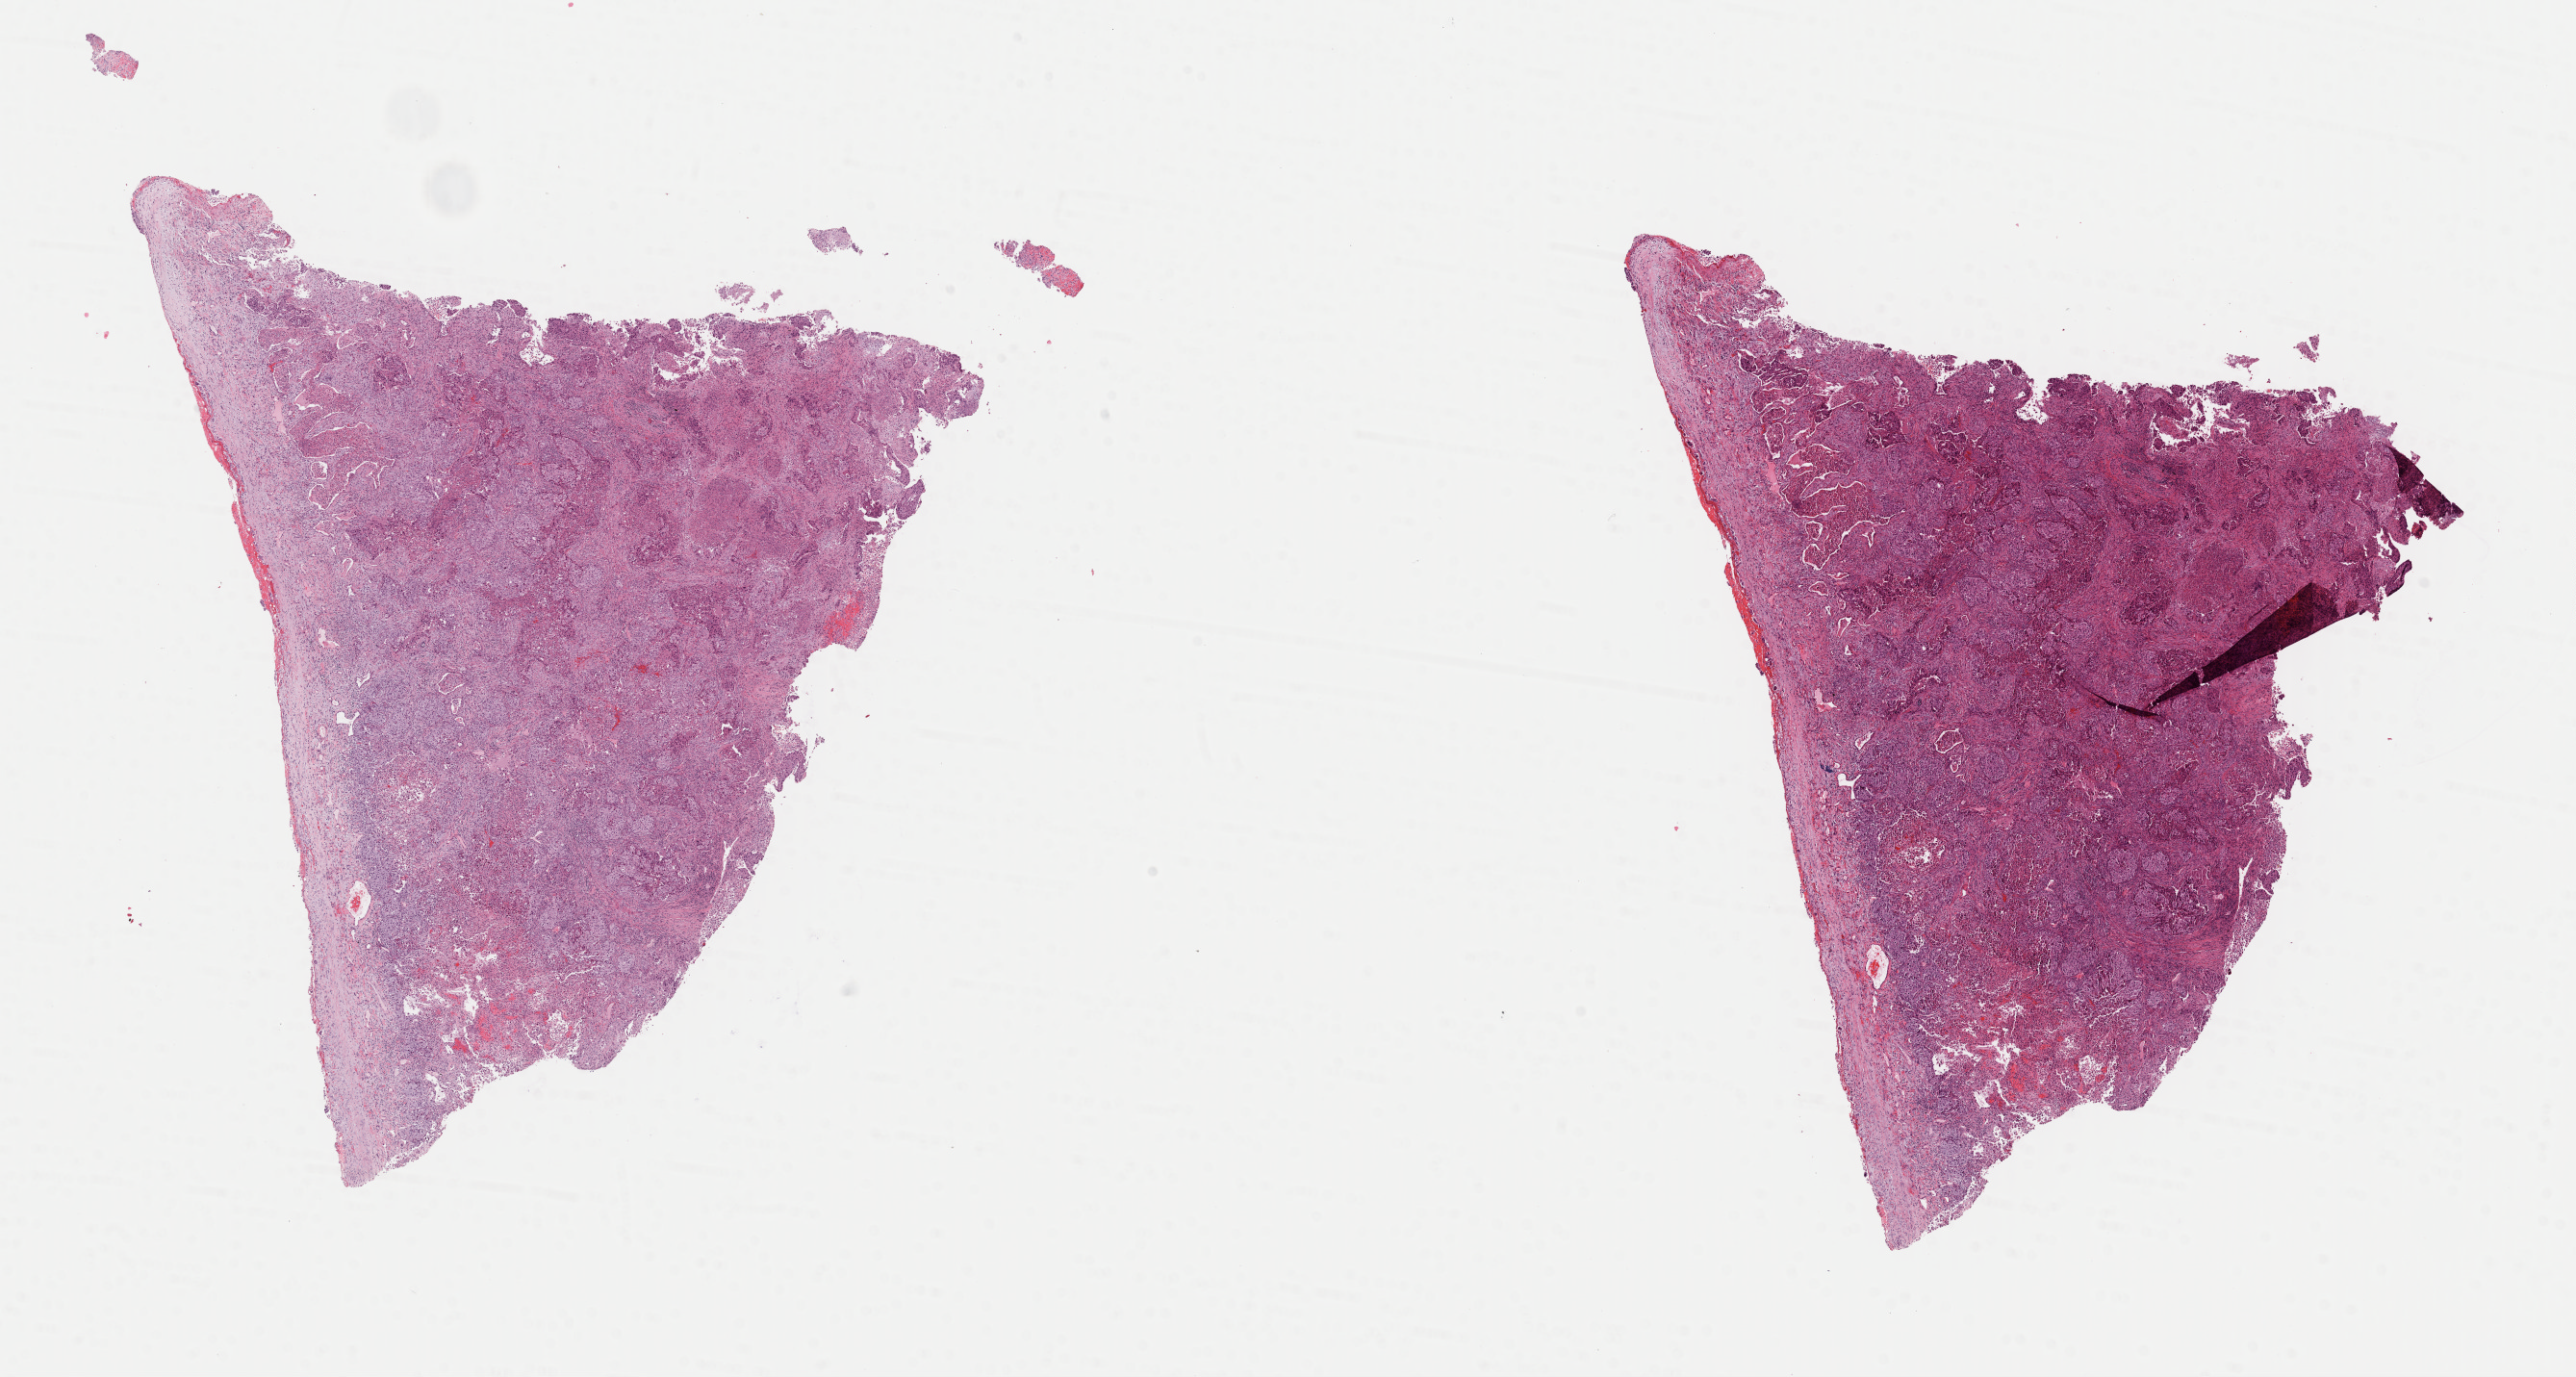
Whole-slide histology image, H&E-stained — a low-resolution overview of the entire scanned area, about 21.1 x 11.3 mm (acquisition: 40x scan); frozen section; lung, primary tumour sample. Male patient; age at initial diagnosis 65 years. Slide review estimates, as recorded: tumour cells 60%, tumour nuclei 70%.
Histologic diagnosis: Adenocarcinoma, NOS (upper lobe, lung).